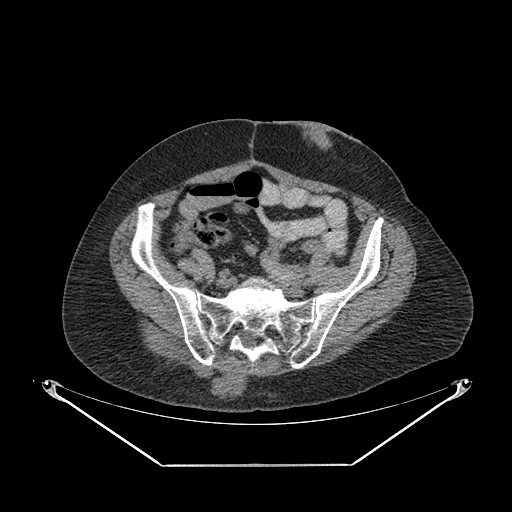
CT of an extremity soft-tissue mass (from a PET/CT study), one axial slice. 140 kVp. Soft-tissue window (W 400 / L 40 HU). 512 × 512 image matrix, field of view 500 × 500 mm. Female patient. From the clinical record (not read from this slice): histological type: spindle cell suggestive of myxofibrosarcoma; grade: intermediate; site of the primary tumour: right buttock.
Annotated regions visible in this slice (expert contour drawn on MRI and transferred to this co-registered scan by the dataset authors):
- gross tumour volume (mass): bounding box [x1, y1, x2, y2] px = [151, 351, 250, 401]